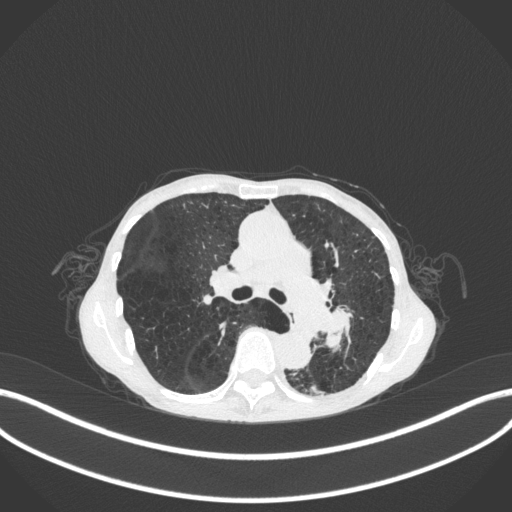
Chest CT, one axial slice. Position 173 of 347 along the scan axis. 120 kVp. Lung window (W 1500 / L -600 HU). 1 mm slice thickness. 512 × 512 image matrix, field of view 400 × 400 mm. Patient: female, 70 years. From the clinical record (not read from this slice): clinical TNM (as recorded): T3 N0 M0.
Structures marked on this image (rectangle marked by the reading radiologist):
- lung tumour (recorded histology: small cell carcinoma): bounding box [x1, y1, x2, y2] px = [320, 299, 361, 365]